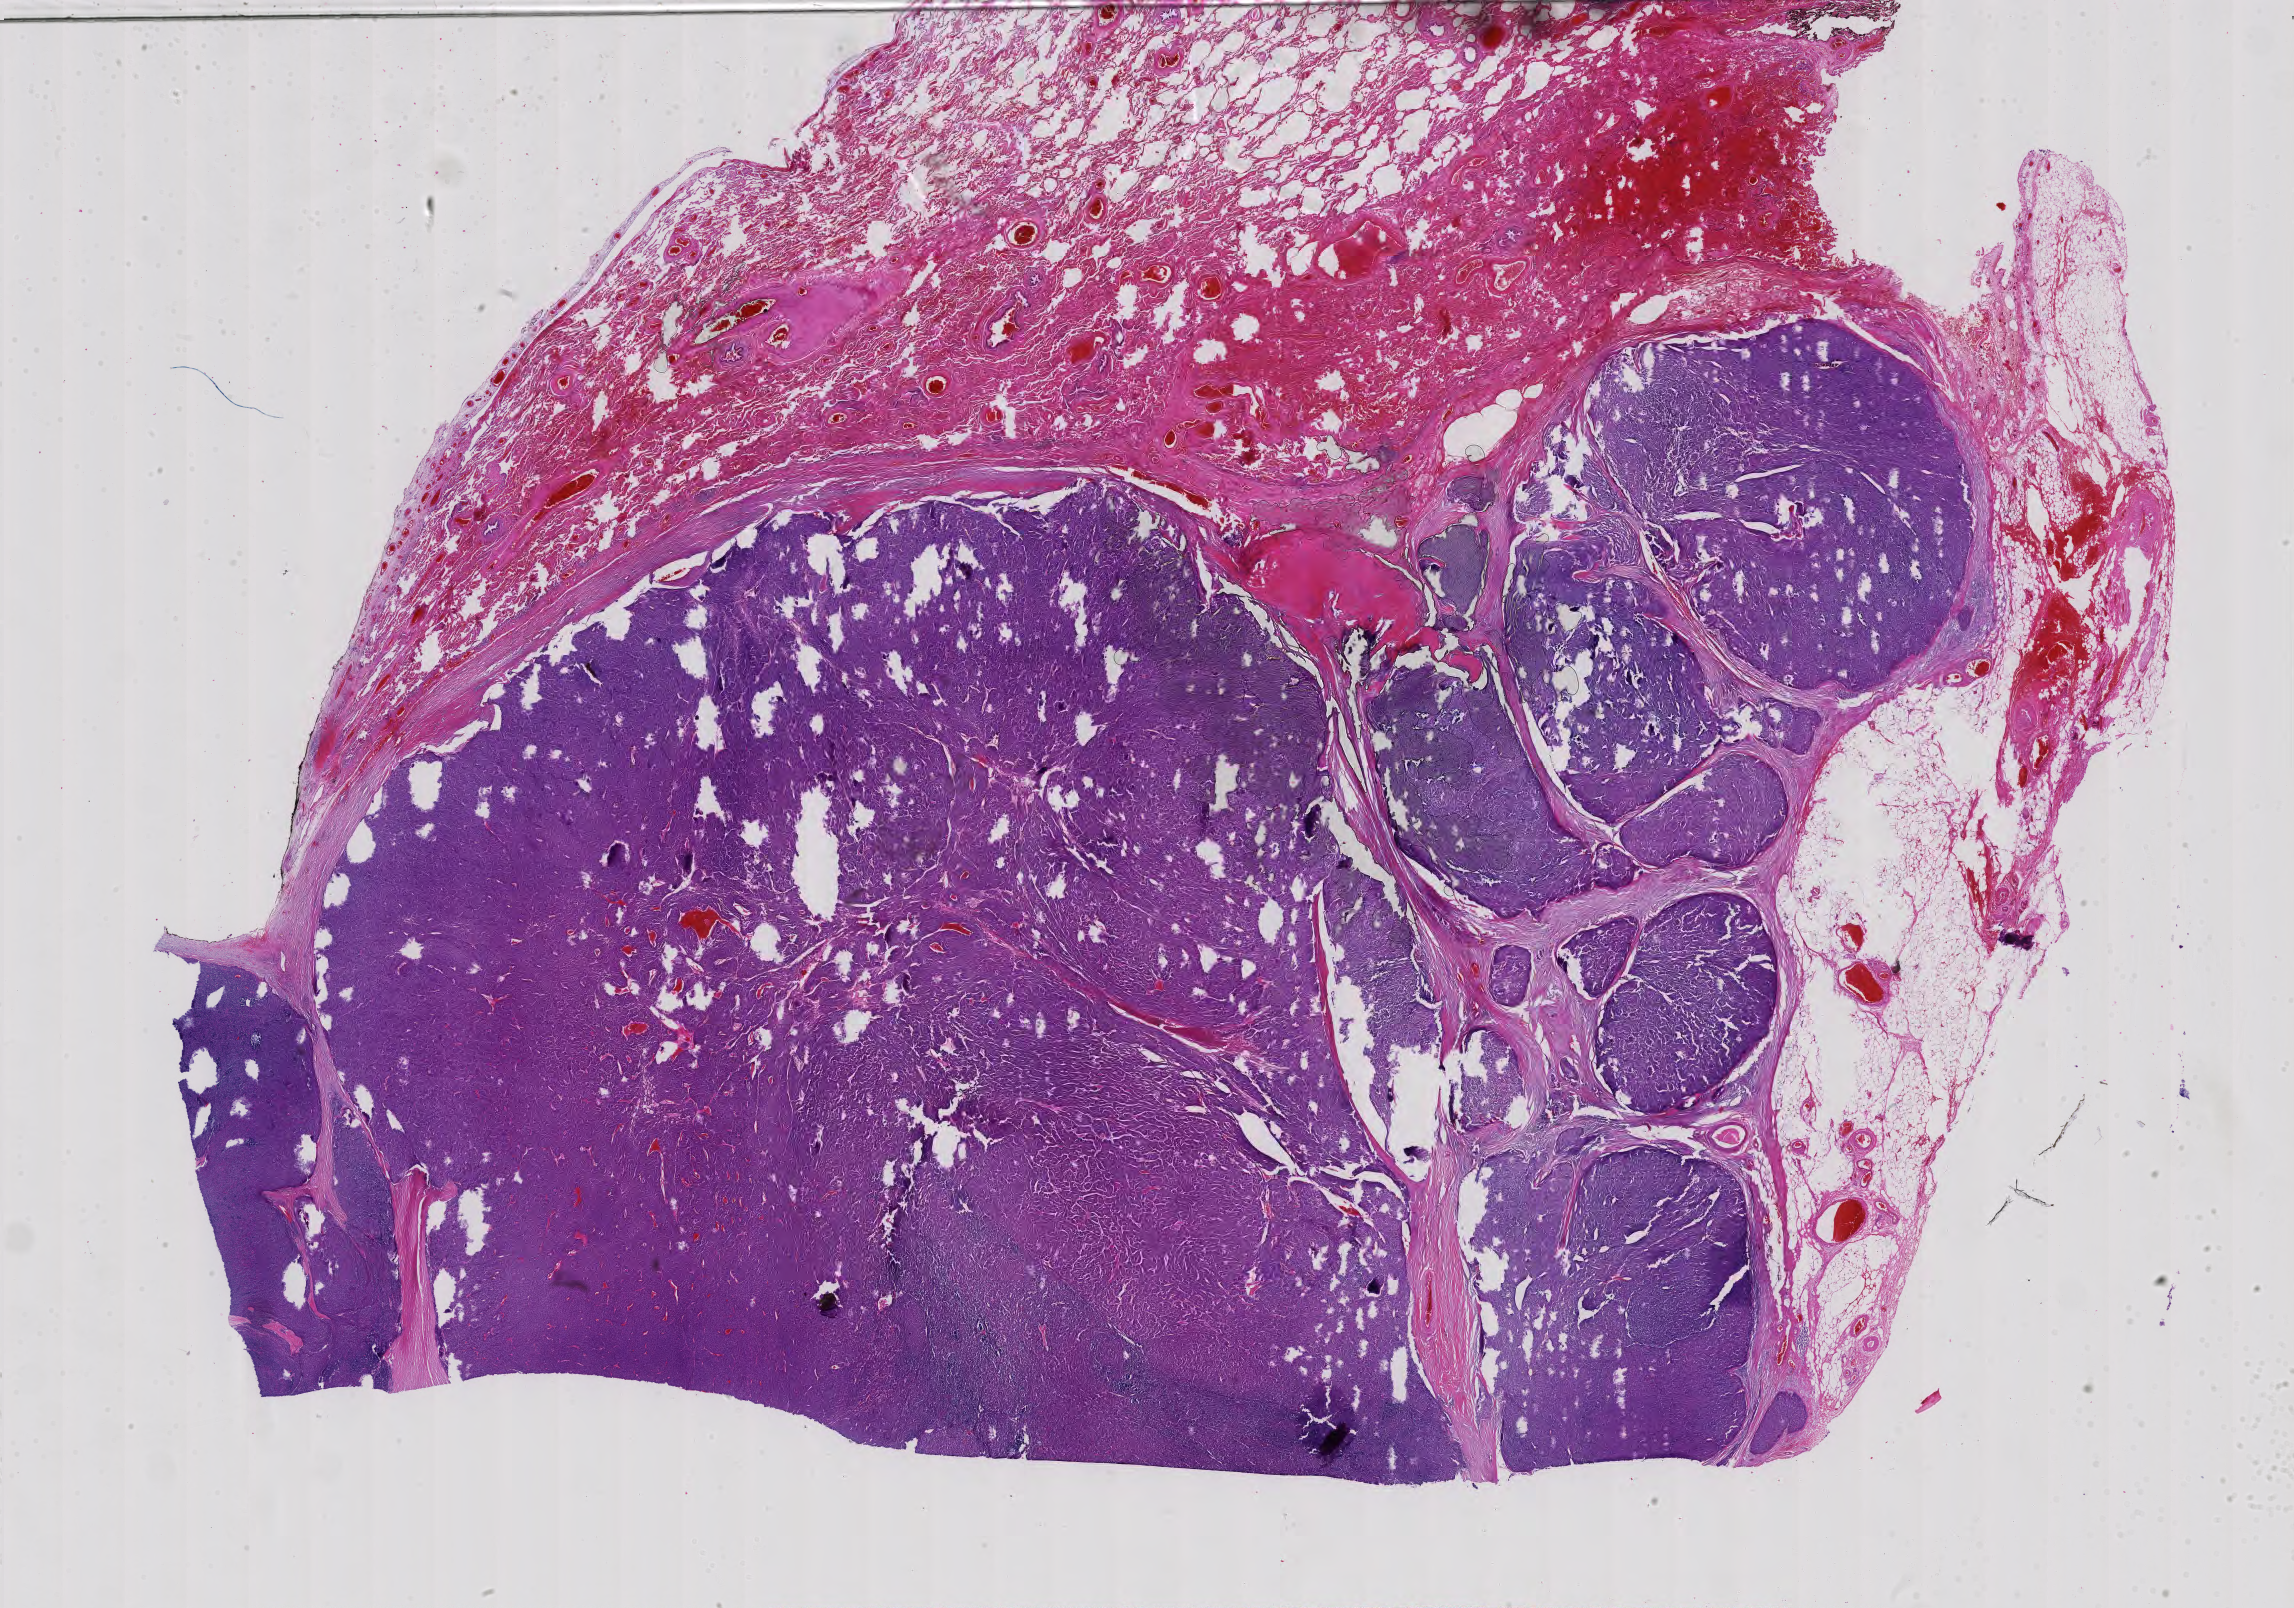
Whole-slide histology image, H&E — a low-resolution overview of the entire scanned area, about 33.5 x 23.5 mm (acquisition: 40x scan); FFPE section; sample: primary tumour, thymus. Female, age 70 years at initial diagnosis.
Pathologic diagnosis: Thymoma, type B3, malignant.